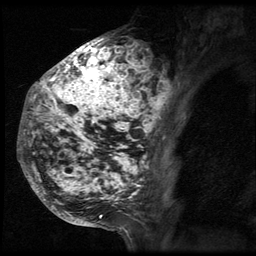
Breast MRI (dynamic contrast-enhanced), one sagittal slice; slice 24 of 64 in the series (ordered by position); 3 images stored at this slice position (order not interpretable as contrast timing); 1.5 T; TE 4.2 ms, TR 9 ms; 256 × 256 image matrix, field of view 180 × 180 mm. Patient: female, 50 years. Case-level facts recorded for this patient, not image findings: setting: breast cancer imaged before/during neoadjuvant chemotherapy; receptor status: triple-negative.
Structures marked on this image (semi-automatic segmentation, software-assisted and operator-edited):
- analysis volume of interest (the breast-tissue region the enhancement analysis was run in; not a lesion): bounding box (x1, y1, x2, y2) in pixels: (24, 39, 174, 212)
- tumour enhancement mask (voxels above the 140 % enhancement threshold inside the analysis volume of interest): (24, 42, 173, 212)